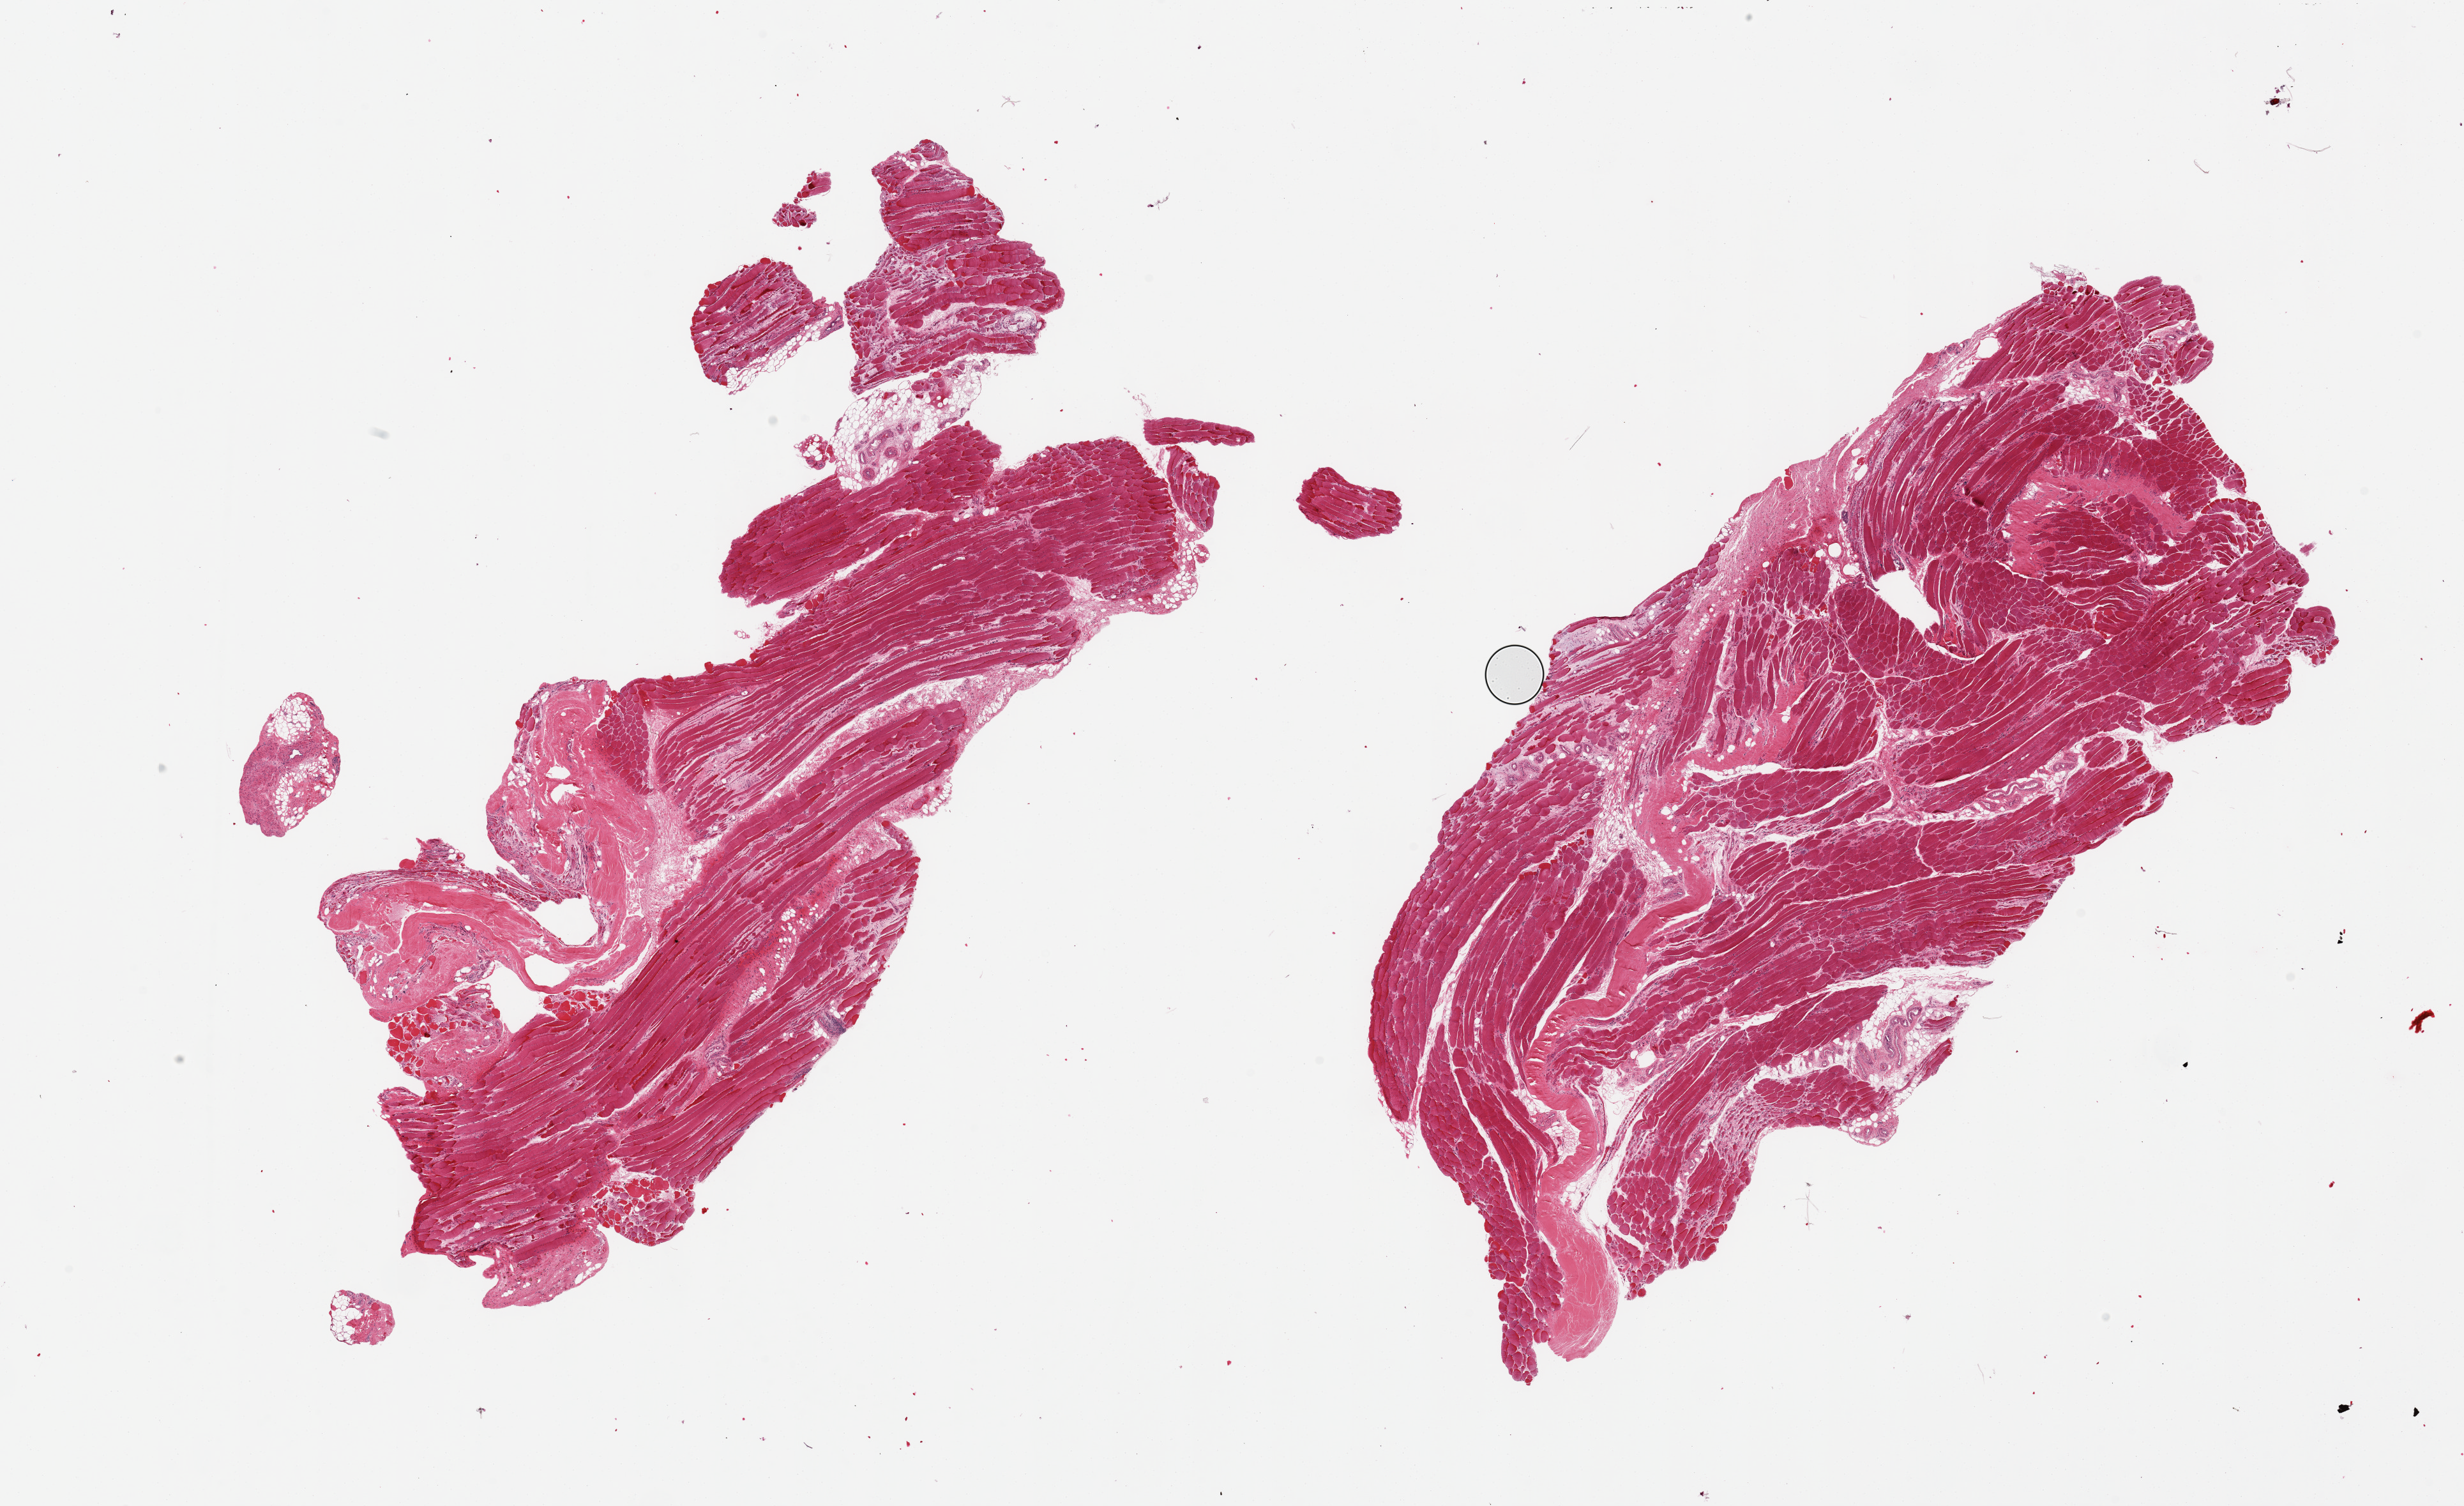
Digitized H&E-stained section — whole scanned area (about 30.5 x 18.6 mm) shown as a low-resolution overview; PAXgene-fixed, paraffin-embedded tissue; section of skeletal muscle (target tissue); tissue donor sample. Donor sex: male.
Pathologist's review note for this sample: 2 pieces. Moderate atrophy with fibrosis and small vessel disease.